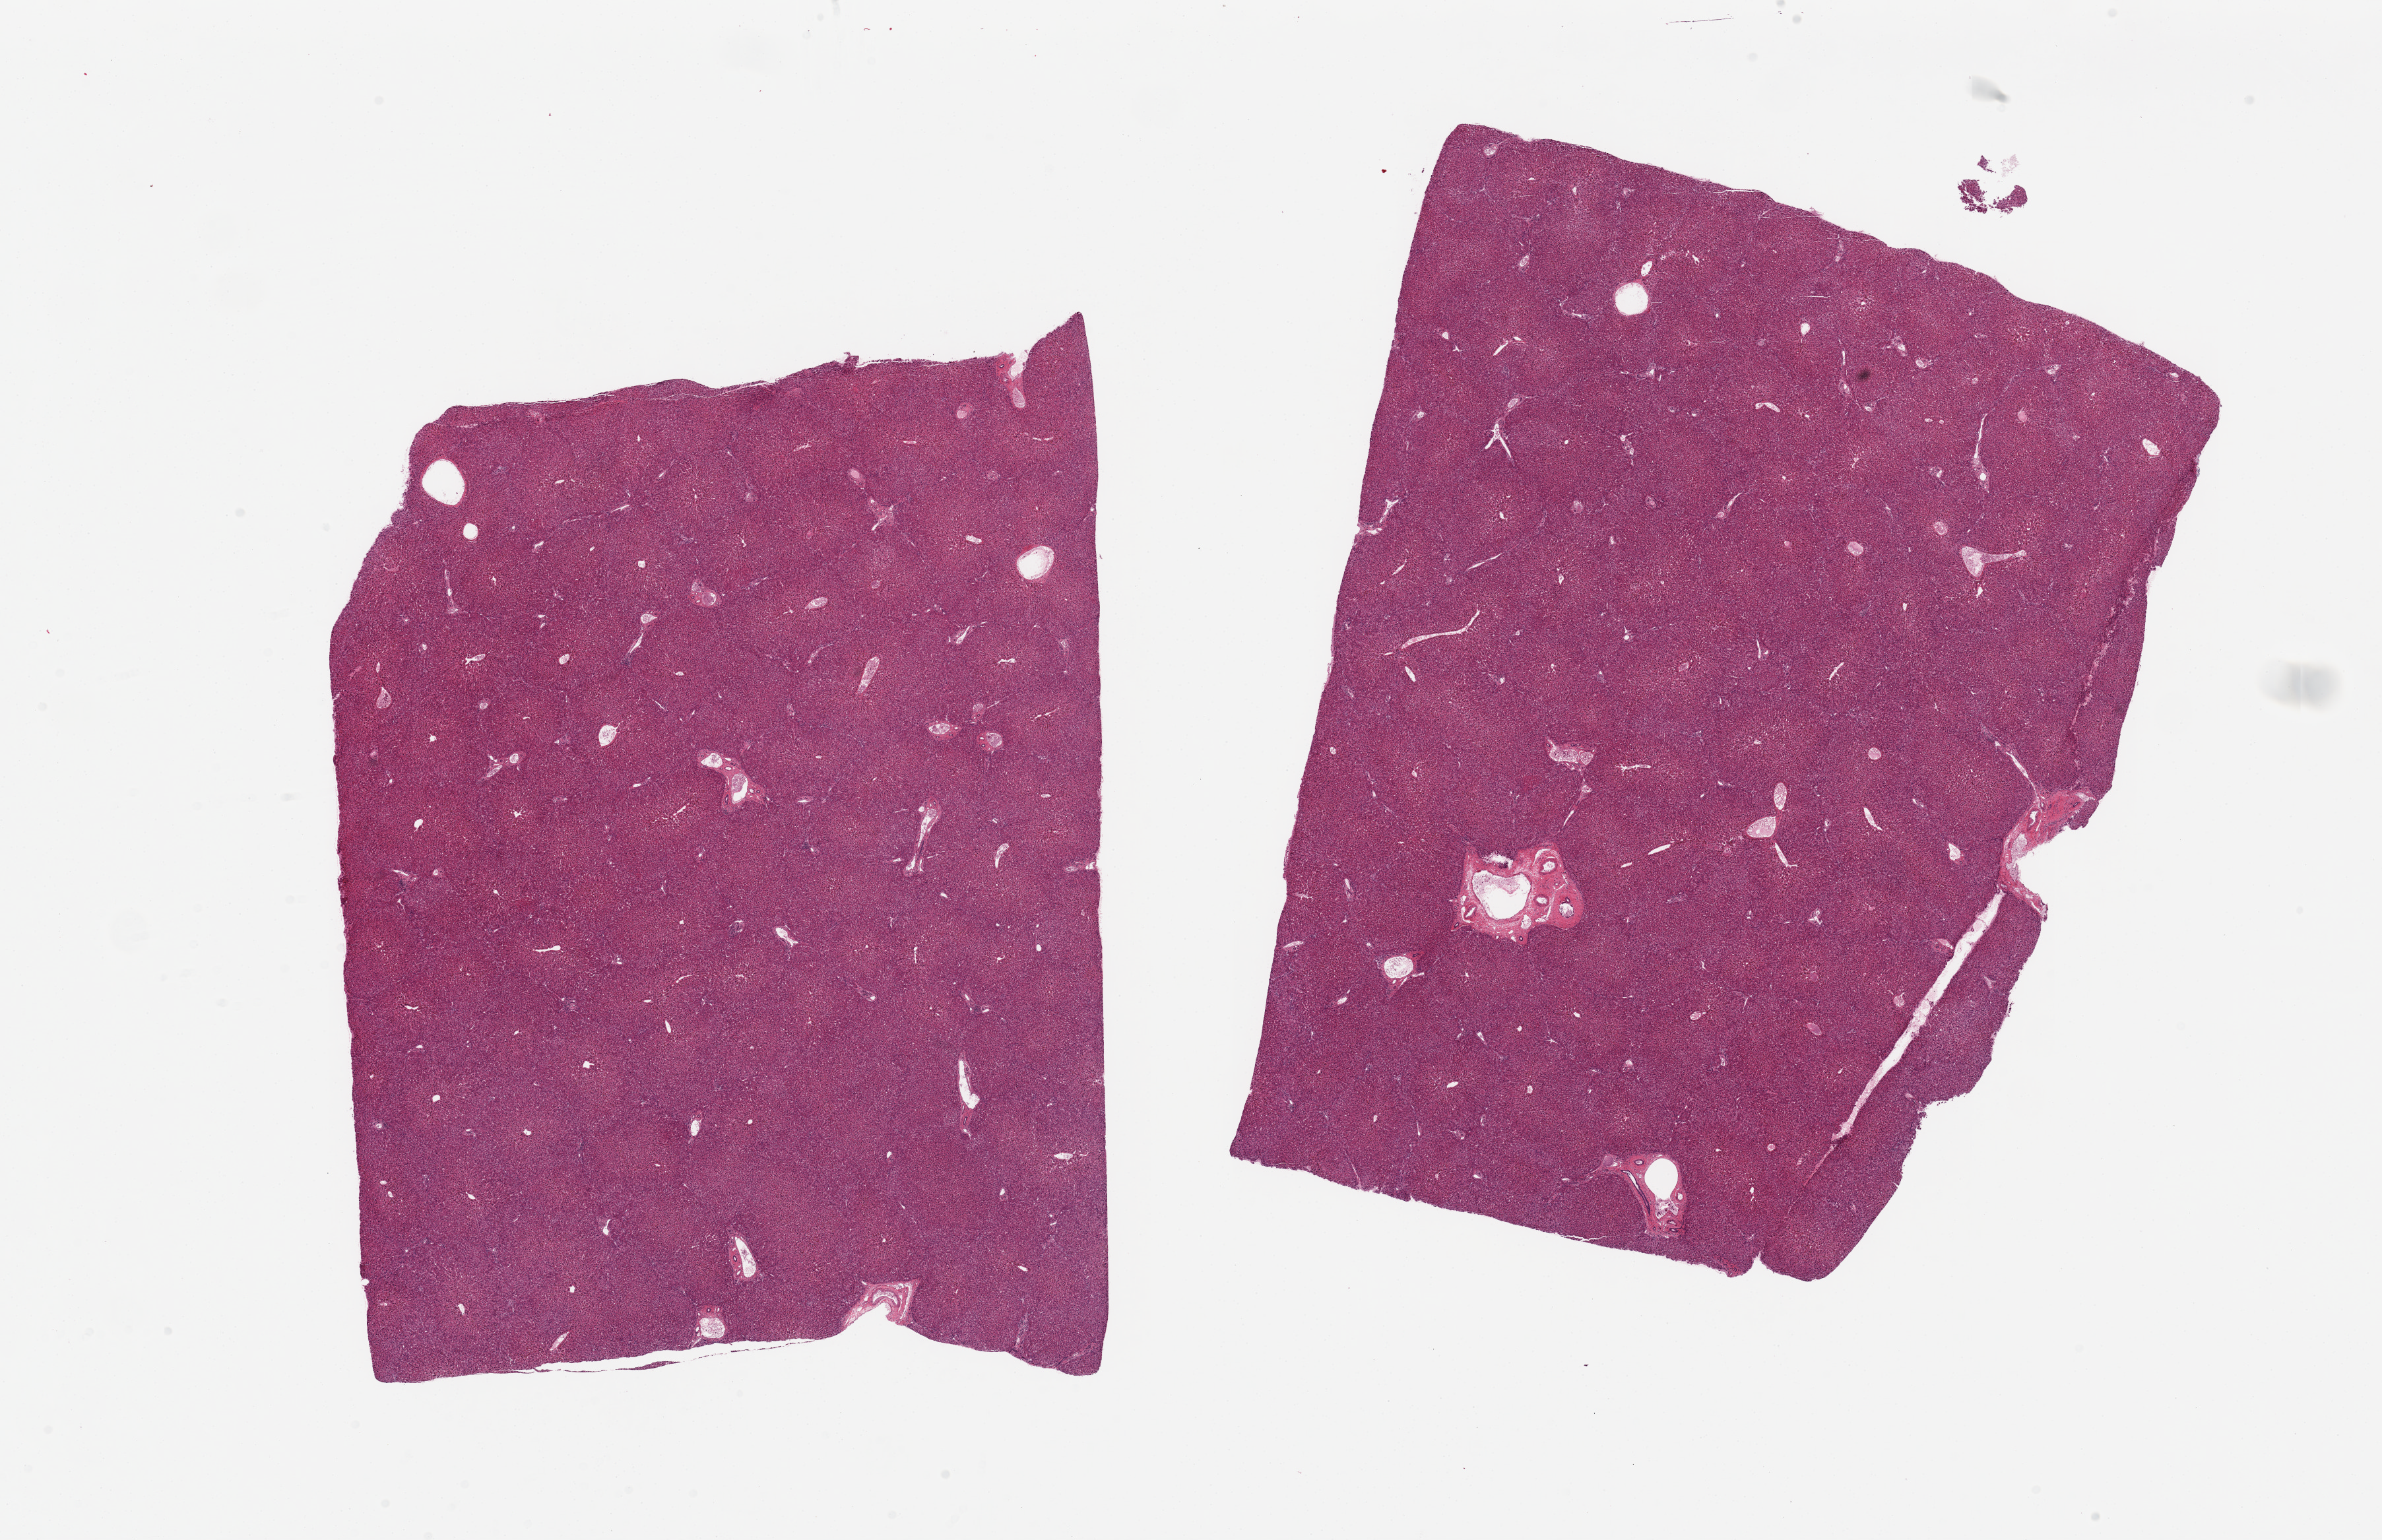
Whole-slide image, H&E stain, brightfield — shown as a low-resolution overview of the whole scanned area (about 28.5 x 18.5 mm), PAXgene-fixed, paraffin-embedded tissue, target tissue: liver, donor tissue sample. Donor sex: female.
* reviewer comment on this tissue sample: 2 pieces. 13x9 & 13x10mm; 70% small droplet variant of macrovesicular steatosis